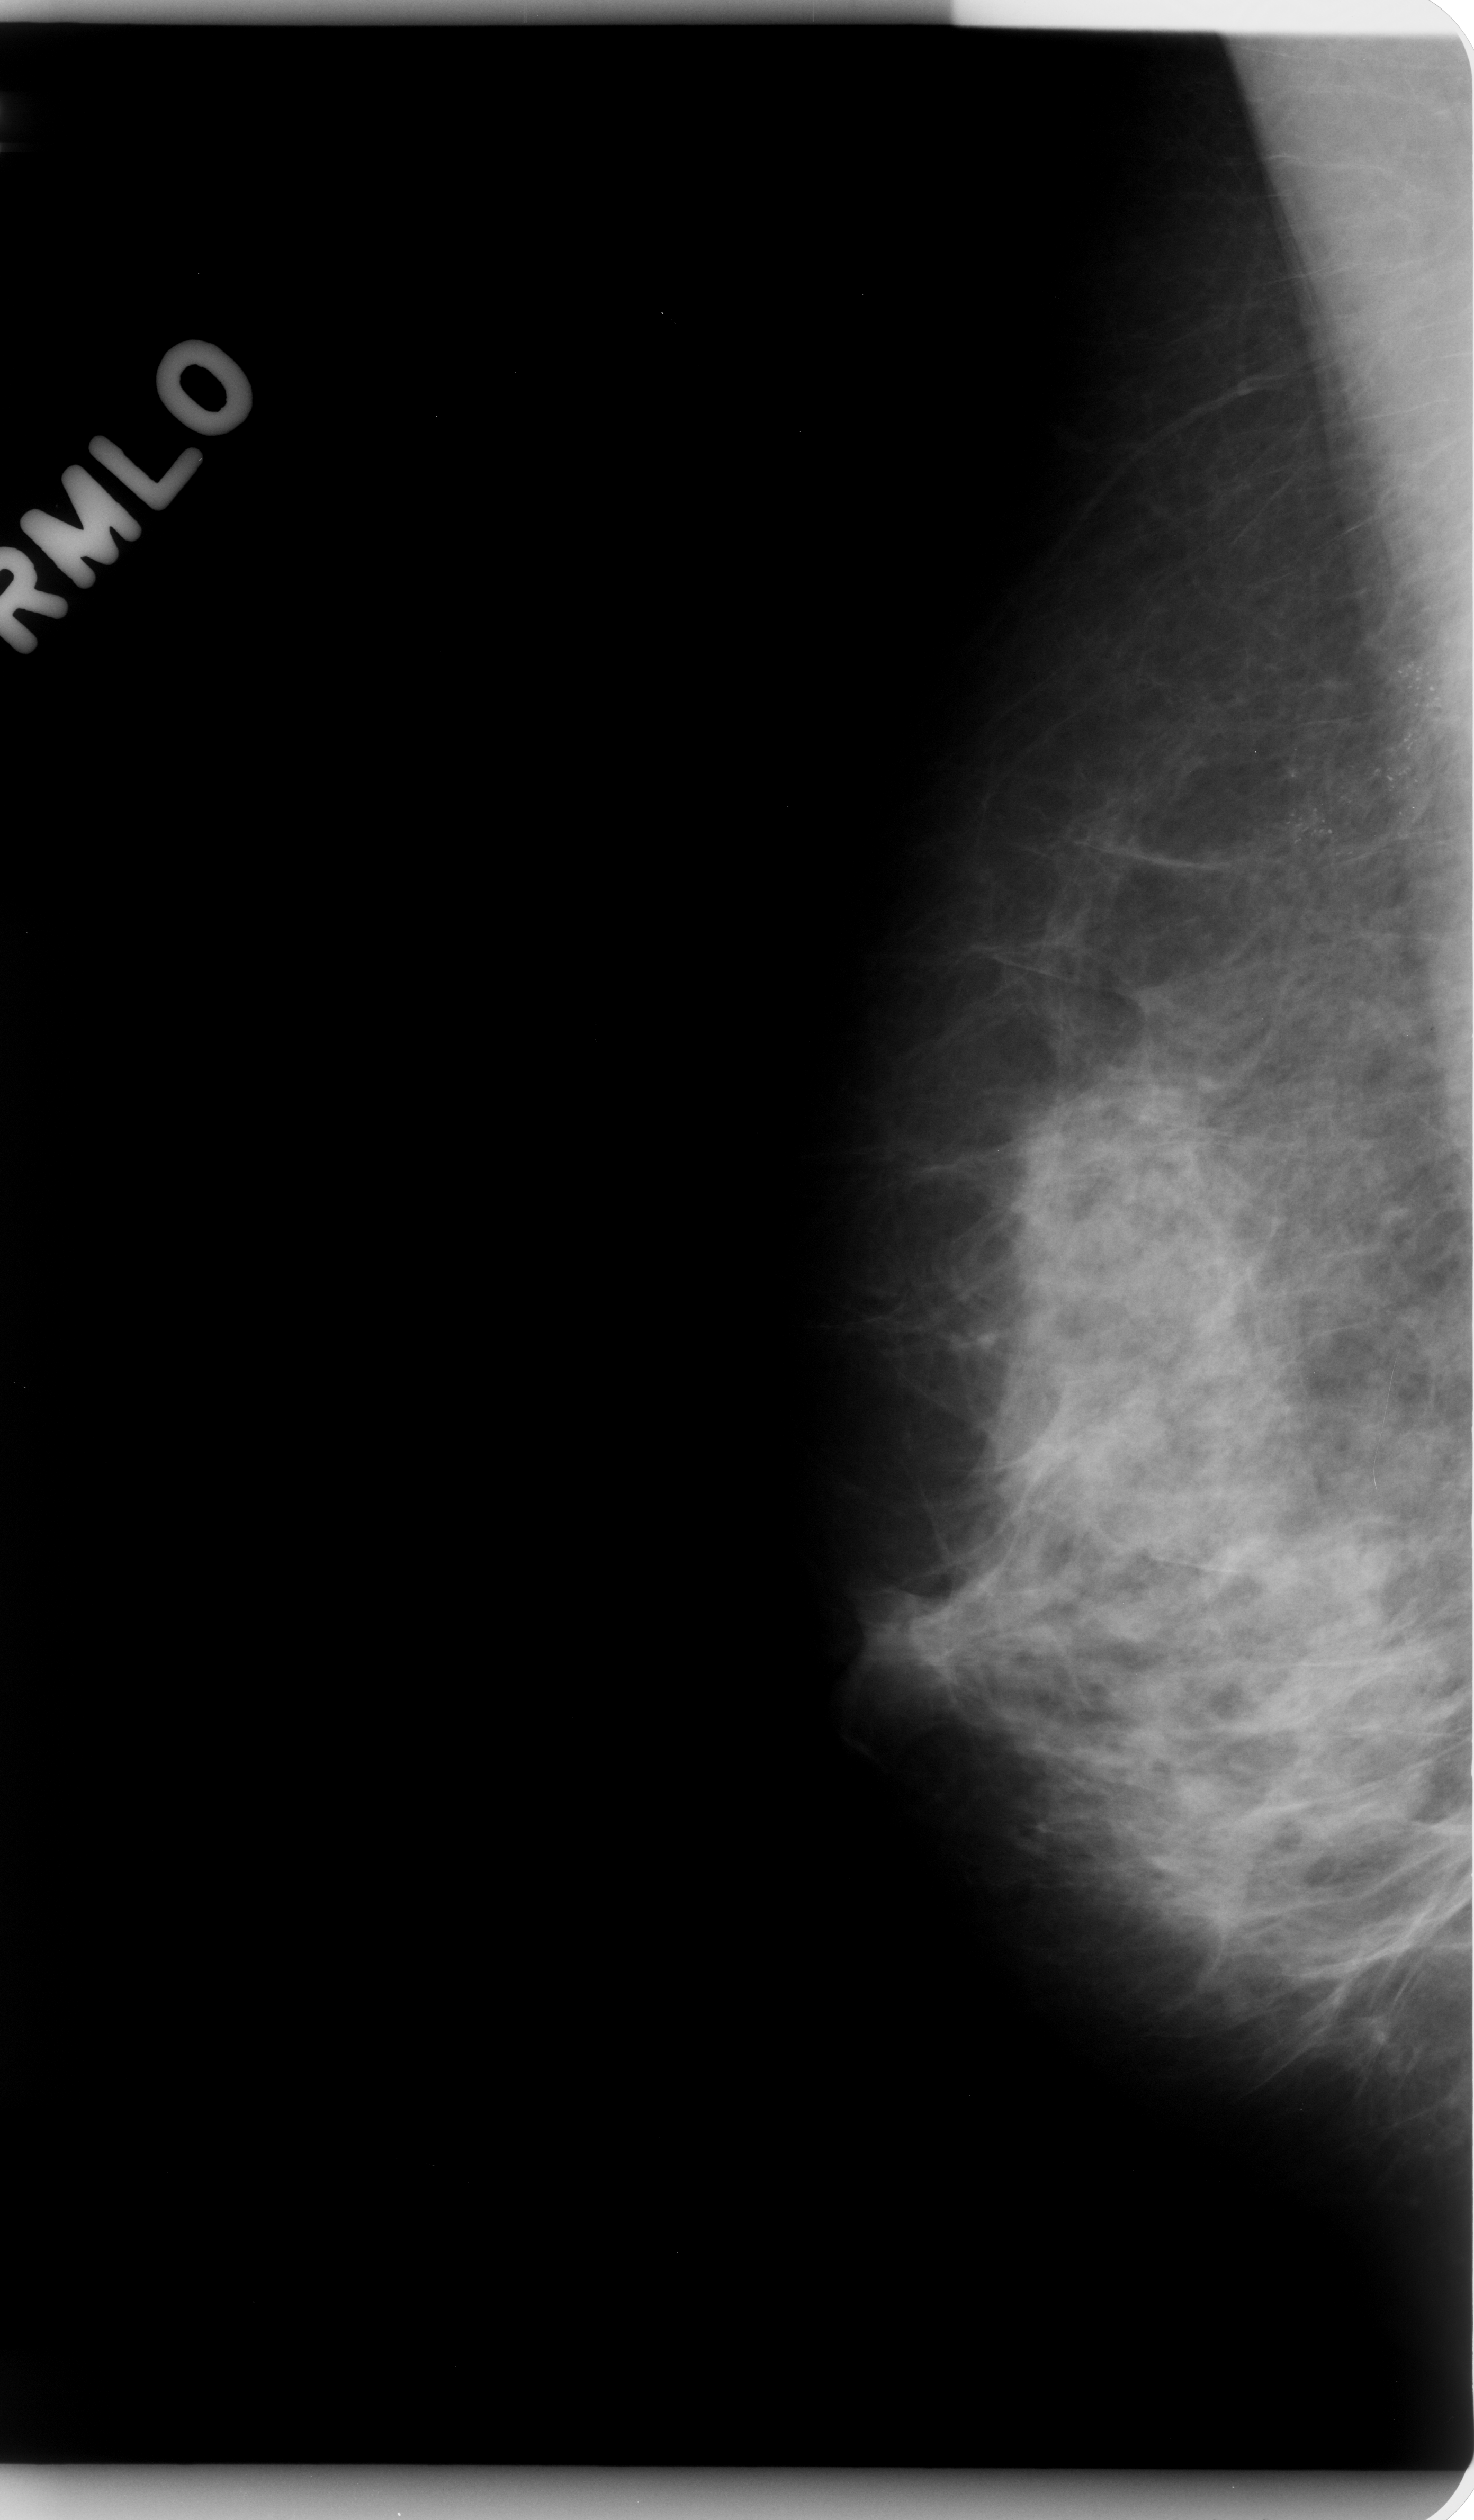
Mammogram (digitized film); right breast; MLO view; breast composition: heterogeneously dense (BI-RADS density category 3 of 4); 1474 × 2520 image matrix.
Marked abnormalities (boxes around the expert regions of interest):
- calcifications, morphology pleomorphic, distribution segmental; BI-RADS assessment category 5; pathology result (as recorded, not read from the image): malignant: box from (x=1025, y=533) to (x=1471, y=1132) px